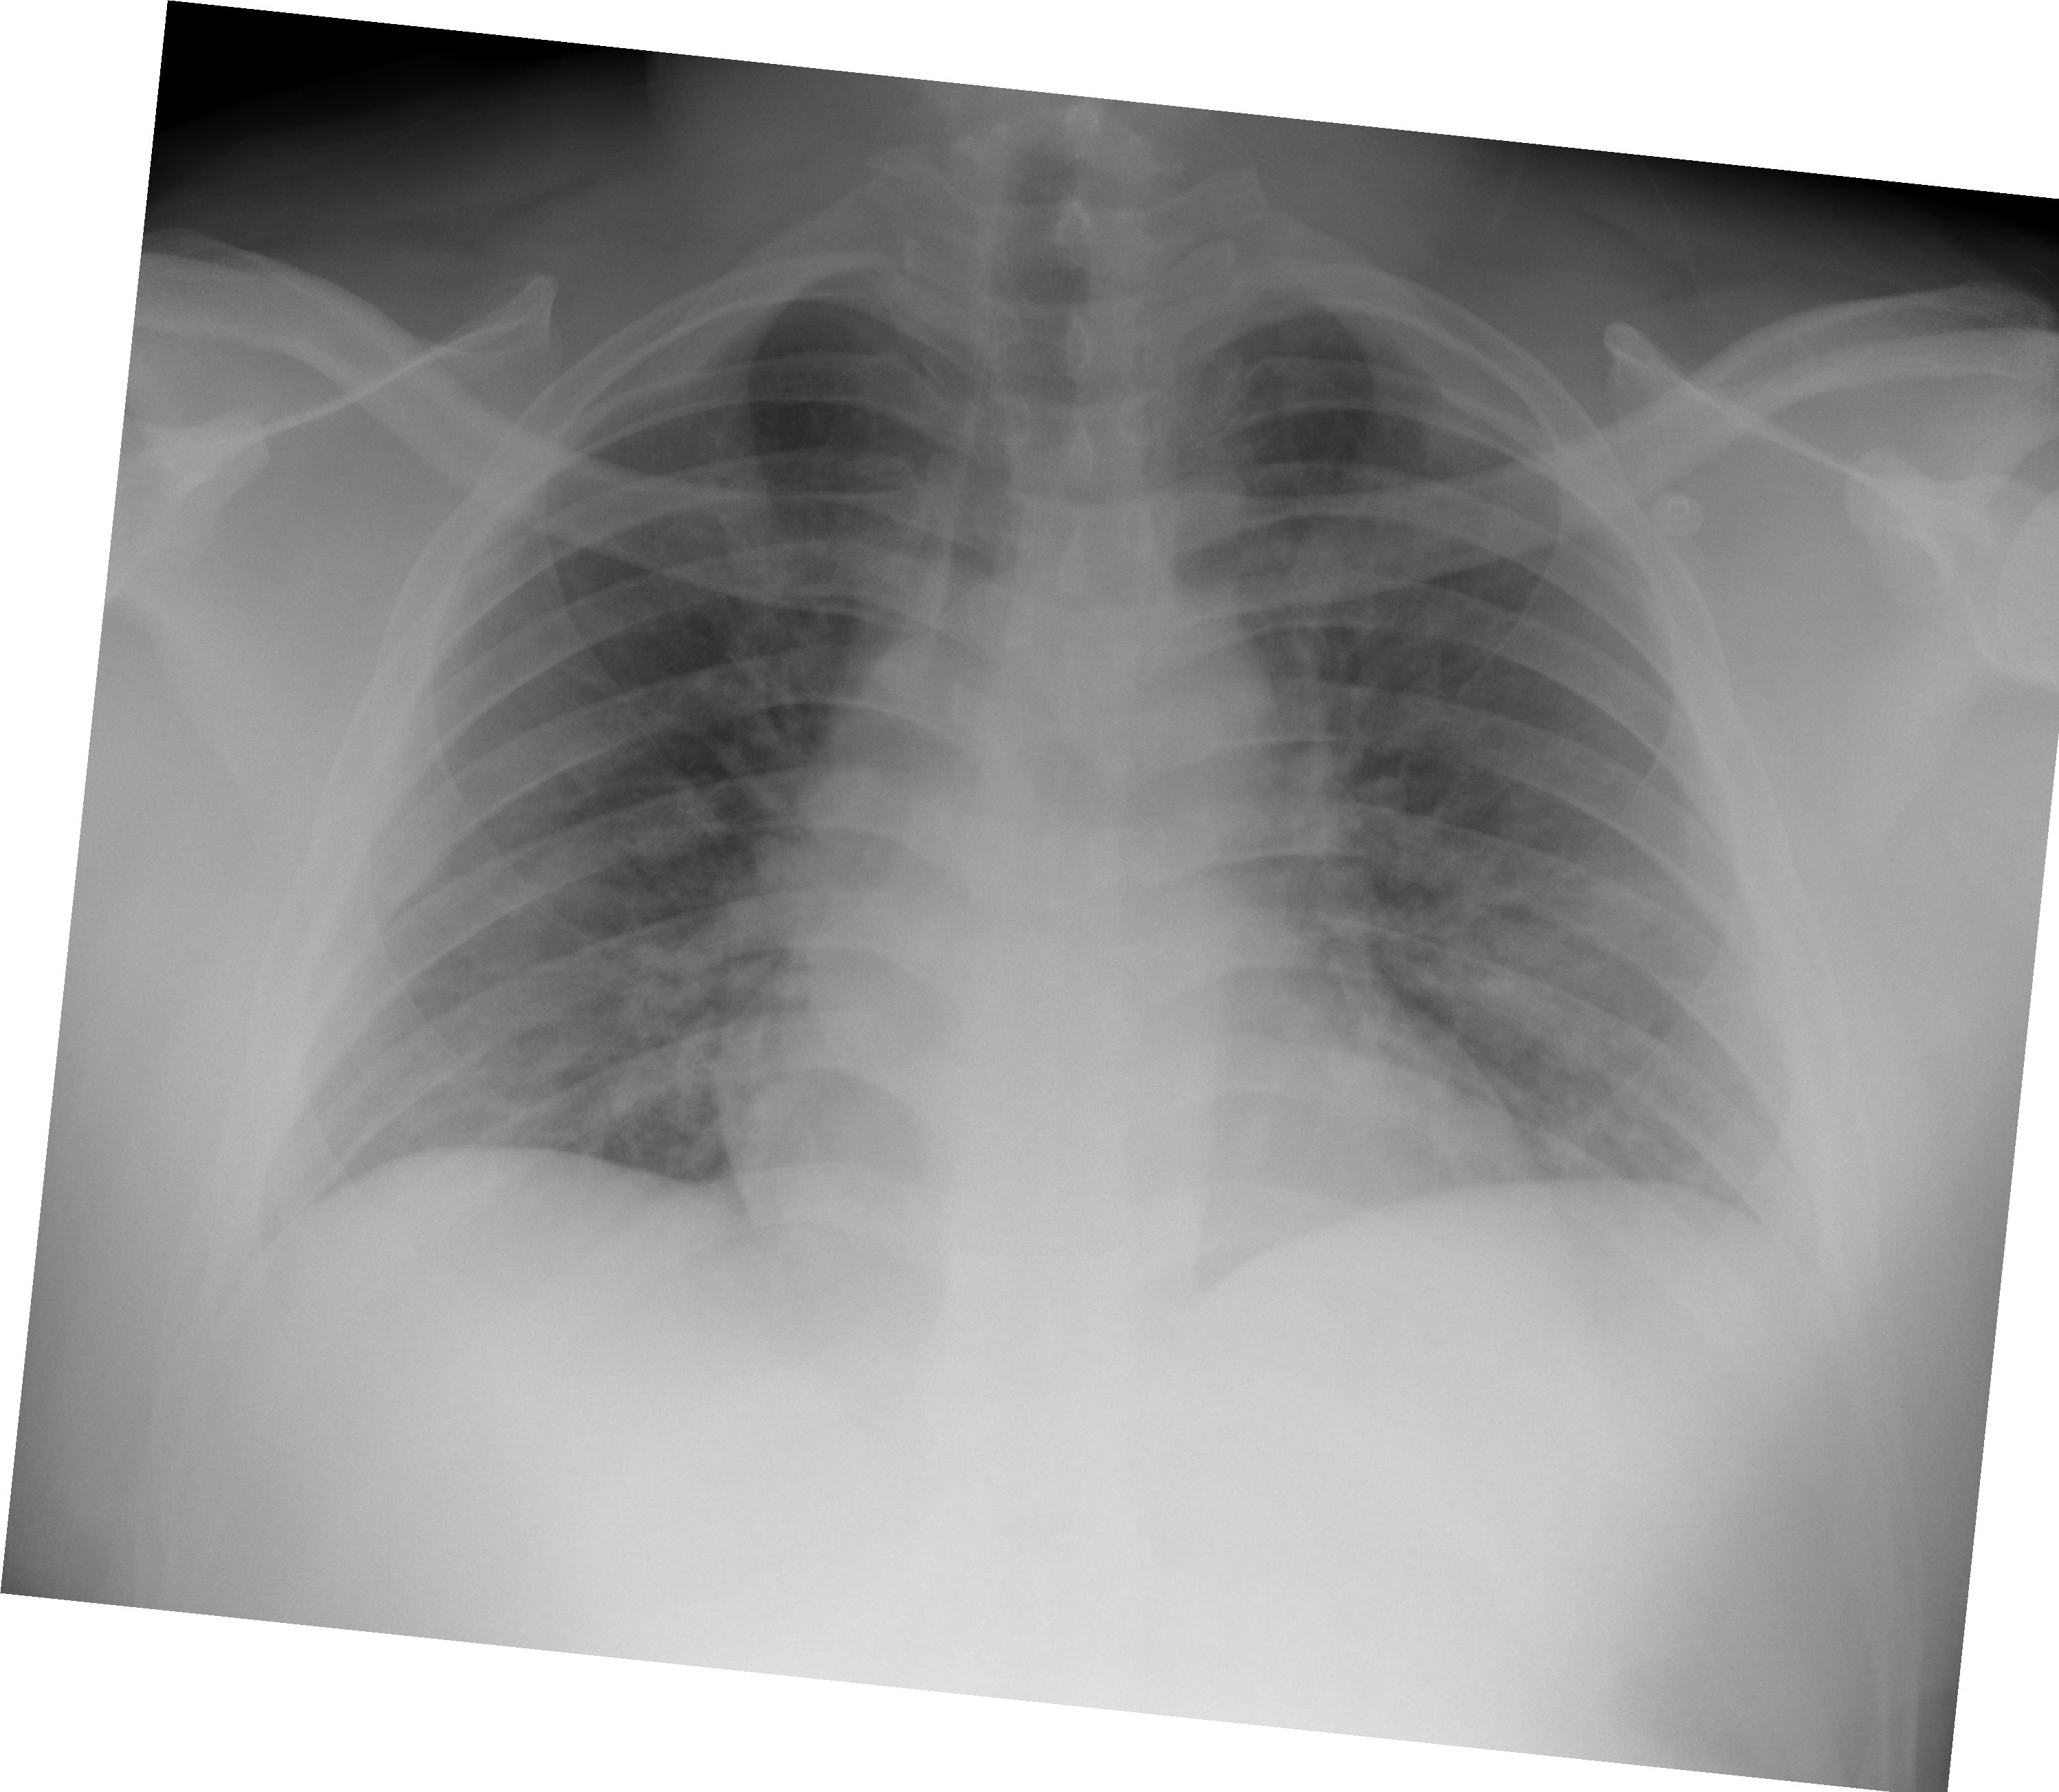
Chest X-ray (portable), AP projection. Male patient, age 36 years; imaged 1 day after the COVID-19 diagnosis.
Radiologist's key findings for this exam: Subtle bibasilar airspace opacities.